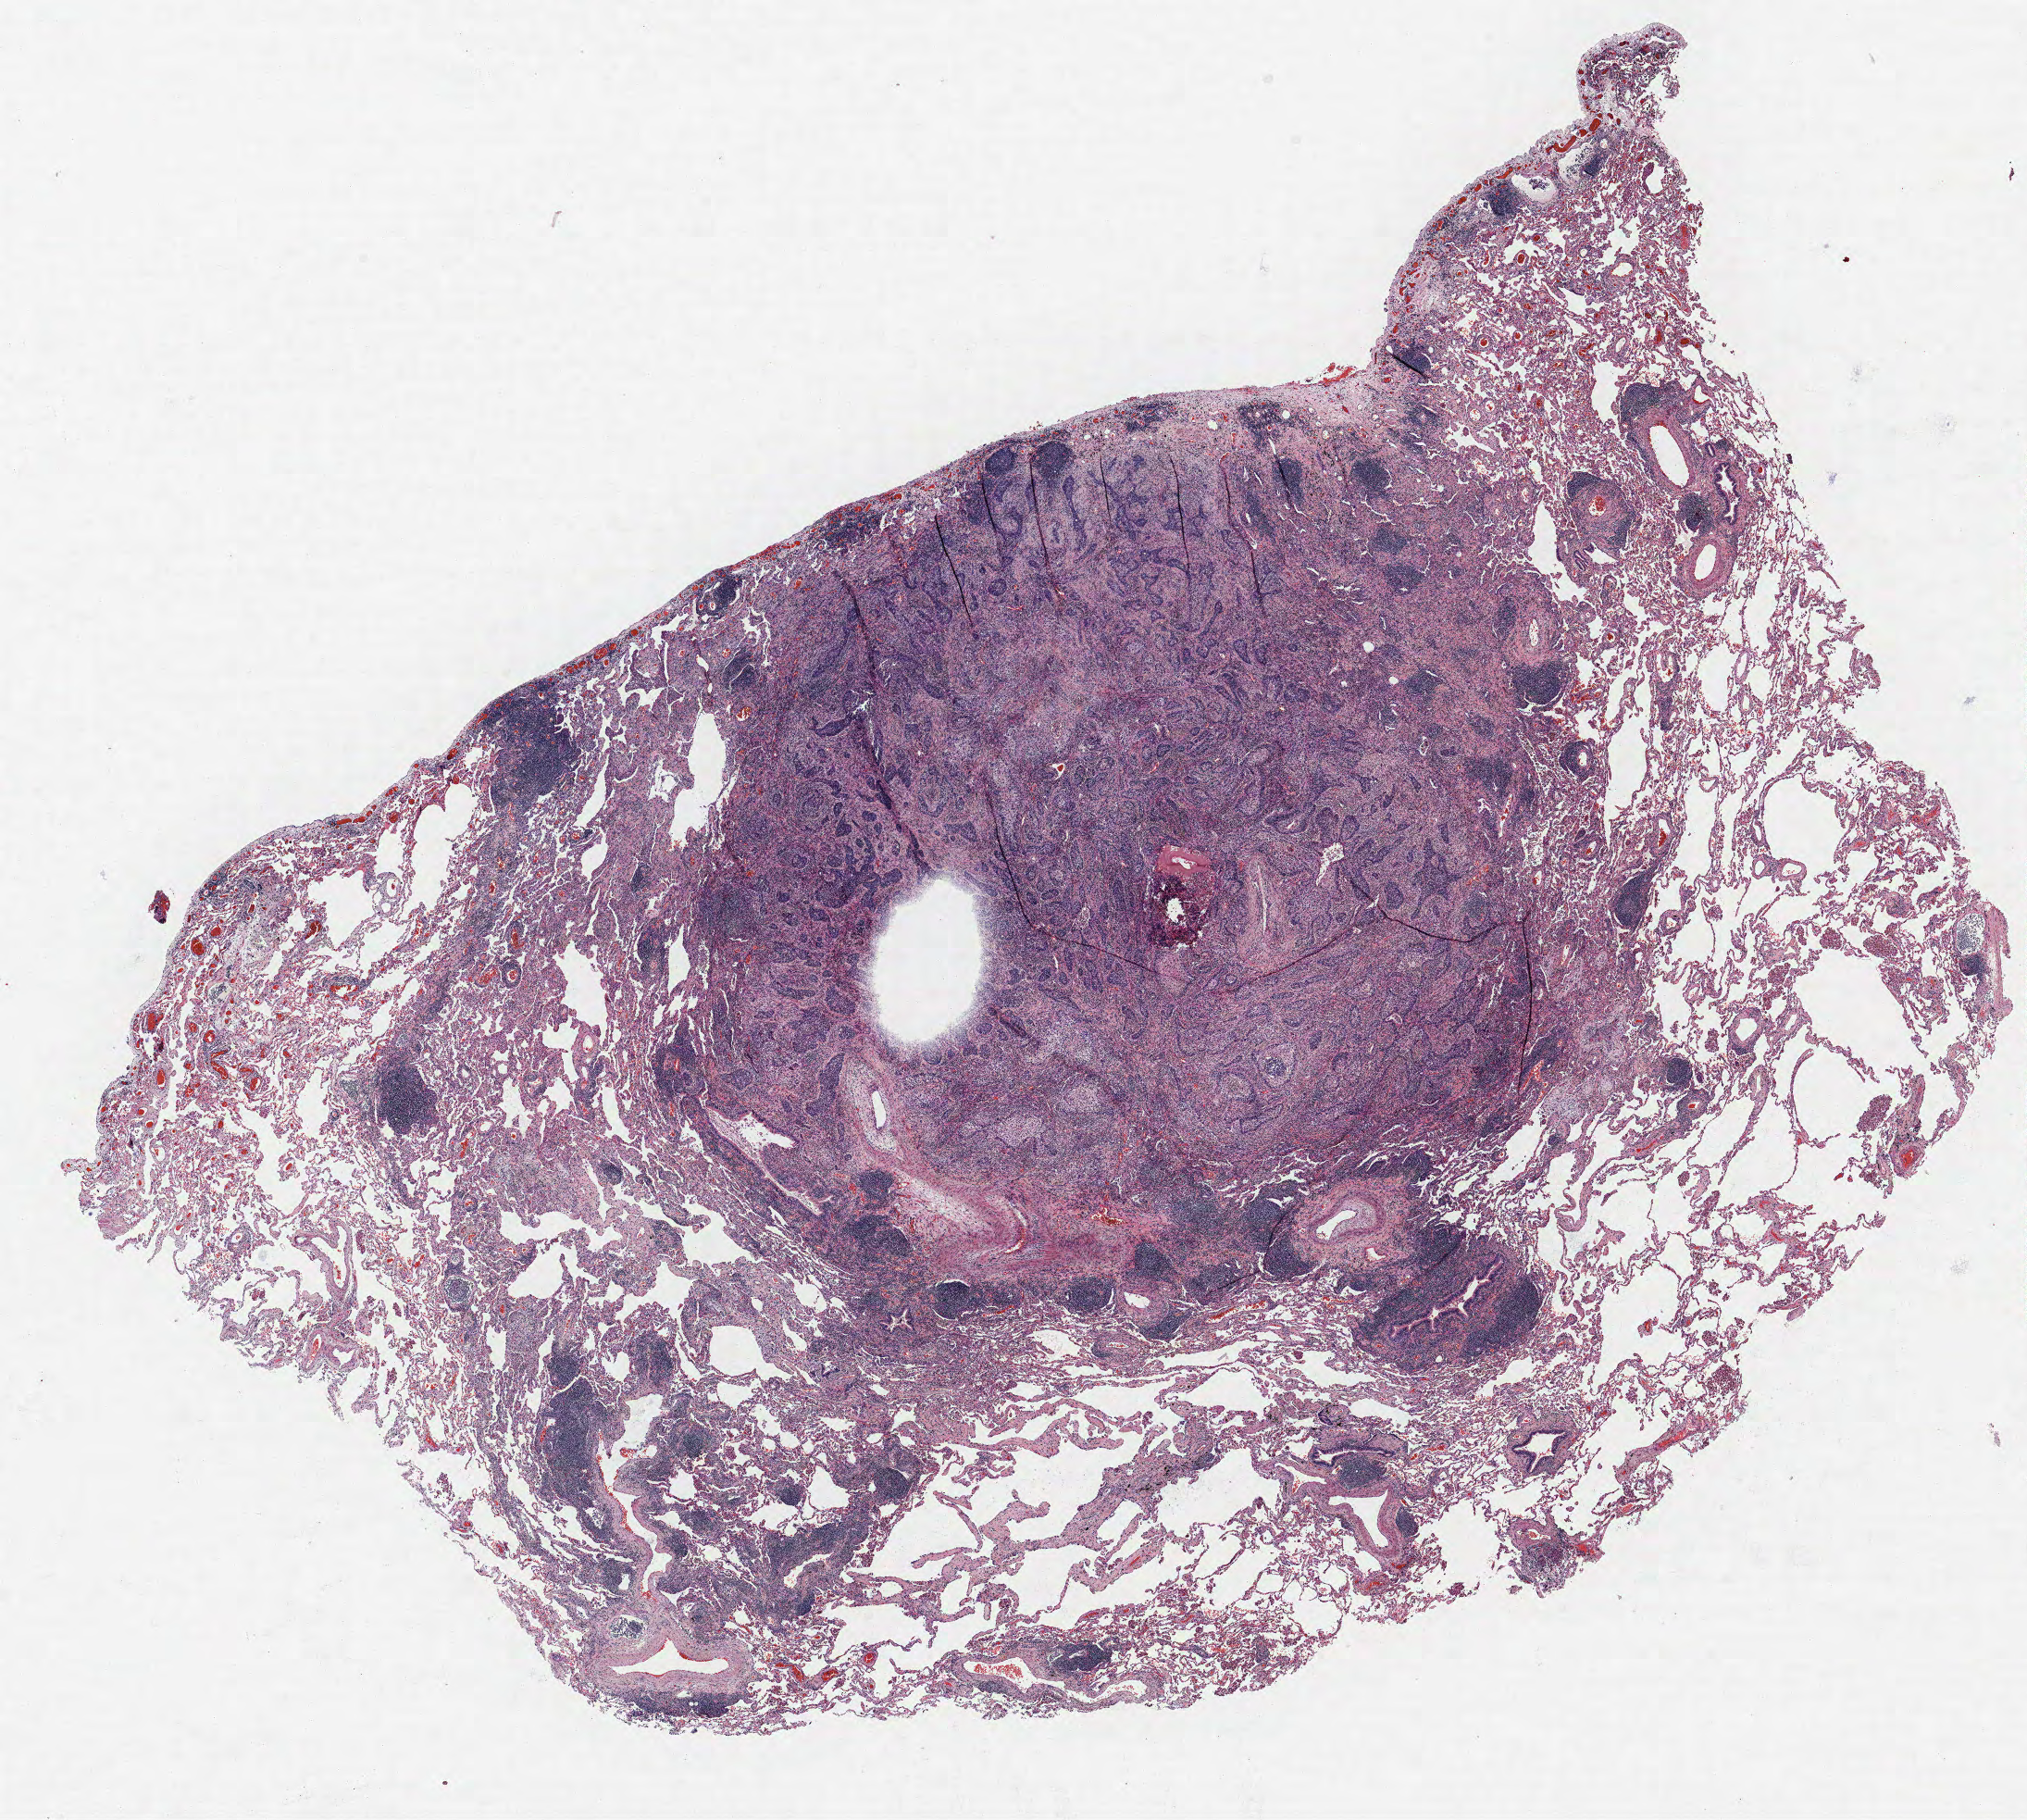
Whole-slide histology image, H&E-stained, whole scanned area (about 17.5 x 15.7 mm) shown as a low-resolution overview; FFPE section; lung tissue. Female patient, aged 56 at enrolment. Grade: moderately differentiated (G2).
* participant's lung-cancer diagnosis: Squamous cell carcinoma, NOS
* primary tumour location (clinical record): right lower lobe
* tumour size (pathology): 17 mm
* stage (AJCC 6th edition): IA